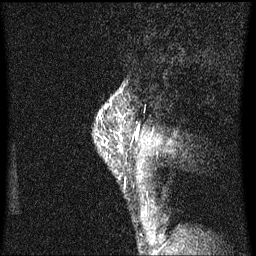
Breast MRI (dynamic contrast-enhanced), one sagittal slice; dynamic contrast-enhanced series, image 2 of 3 at this slice position (ordered by acquisition); 1.5 T; TE 4.2 ms, TR 8.4 ms; 2 mm slice thickness; 256 × 256 image matrix, field of view 200 × 200 mm. Patient: female, 40 years.
Outlined on this slice (semi-automatic segmentation, software-assisted and operator-edited):
- analysis volume of interest (the breast-tissue region the enhancement analysis was run in; not a lesion): bounding box [x1, y1, x2, y2] px = [101, 104, 127, 185]
- tumour enhancement mask (voxels above the 70 % enhancement threshold inside the analysis volume of interest): [101, 114, 123, 151]